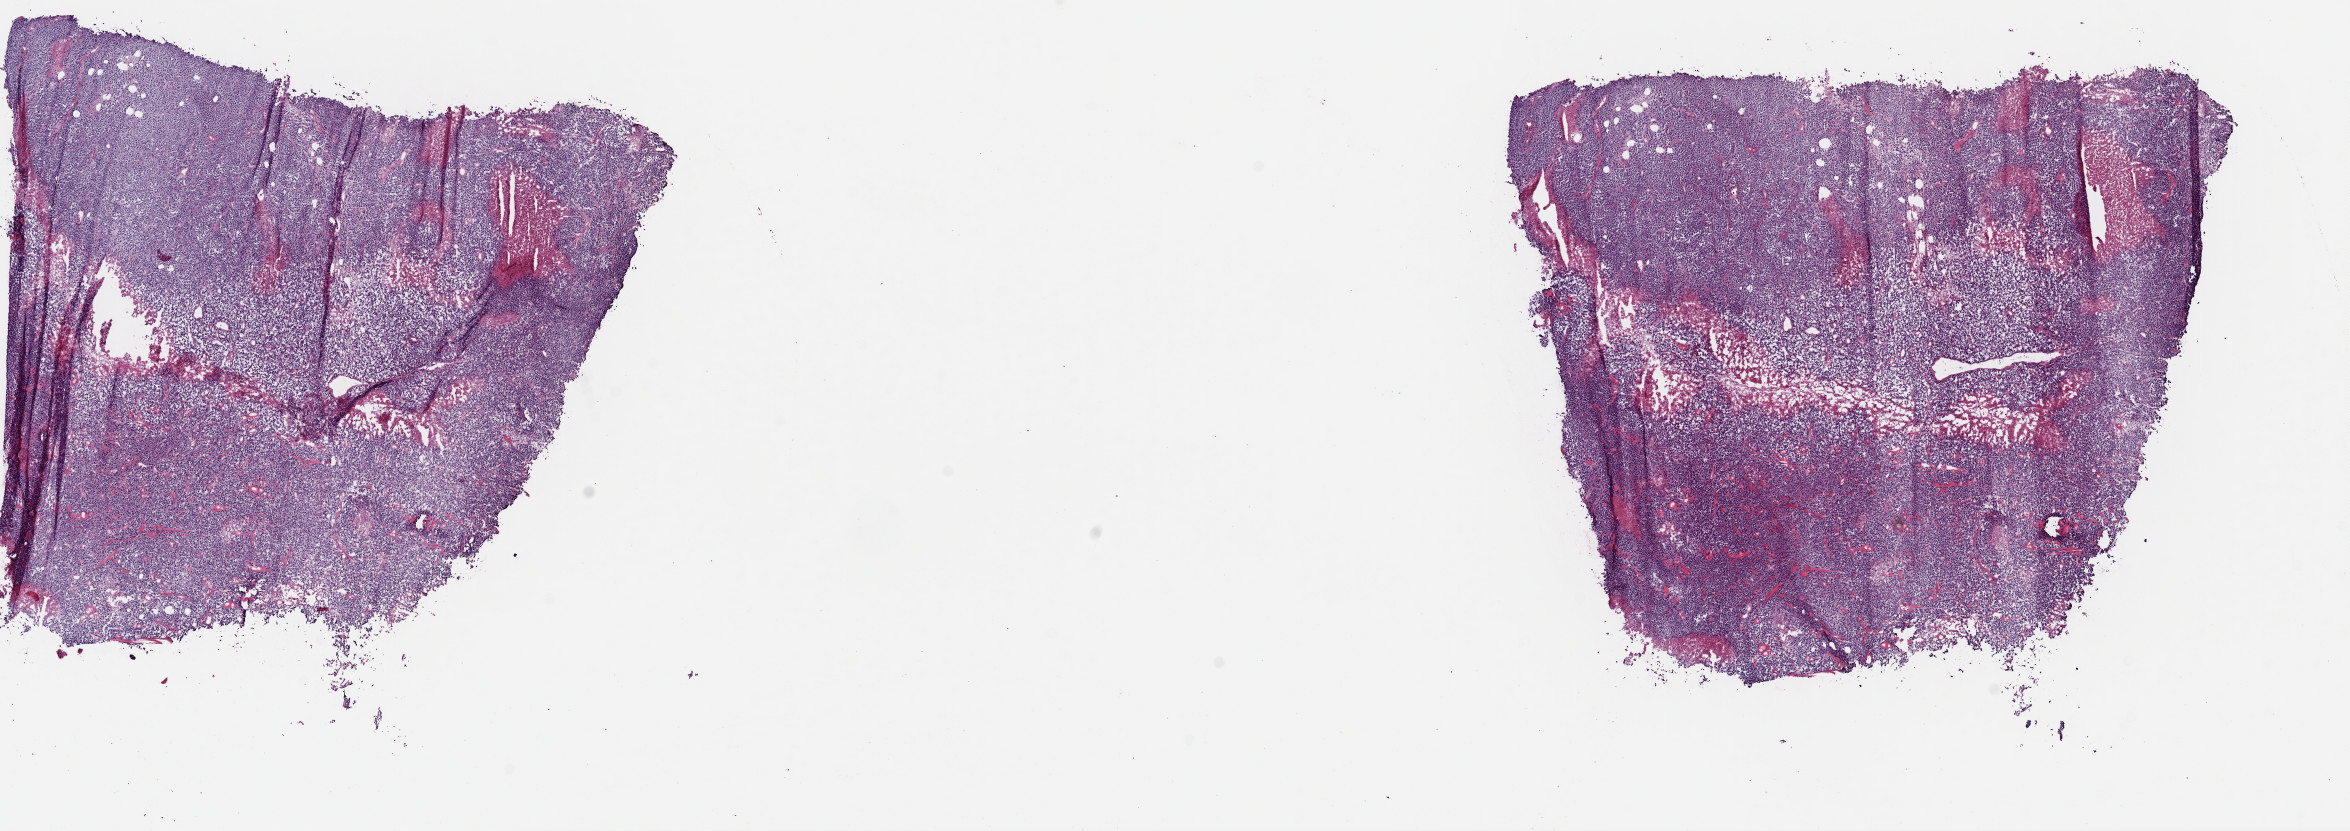
H&E-stained whole-slide image — whole scanned area (about 18.6 x 6.6 mm, acquisition: 40x scan) shown as a low-resolution overview, frozen section, metastatic tumour sample, sampled site not recorded. Male patient; age at initial diagnosis 59 years. Slide review estimates, as recorded: tumour cells 95%, tumour nuclei 95%, normal cells 0%, stromal cells 0%, necrosis 5%. Inflammatory infiltration, as recorded: lymphocyte infiltration 0%, monocyte infiltration 0%, neutrophil infiltration 0%.
• this section: metastatic tumour tissue
• patient diagnosis: Malignant melanoma, NOS